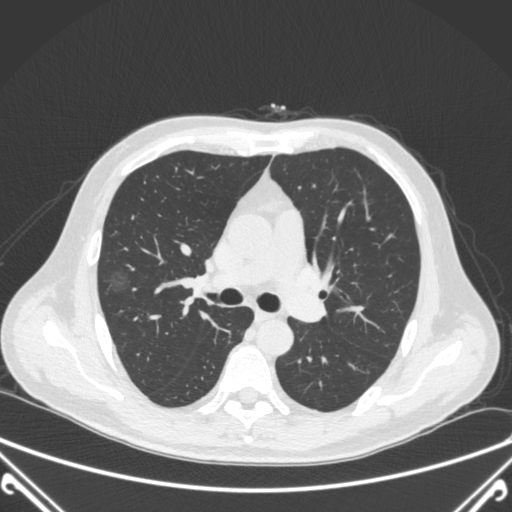
Chest CT, one axial slice. Slice 228 of 360 in the series (ordered by position). 120 kVp. Lung window (W 1500 / L -600 HU). 512 × 512 image matrix, field of view 380 × 380 mm. Male patient, age 64 years. From the clinical record (not read from this slice): clinical TNM (as recorded): T1c N0 M0; histopathological grade: G2.
Outlined on this slice (rectangle marked by the reading radiologist):
- lung tumour (recorded histology: adenocarcinoma): bounding box (x1, y1, x2, y2) in pixels: (98, 265, 137, 302)